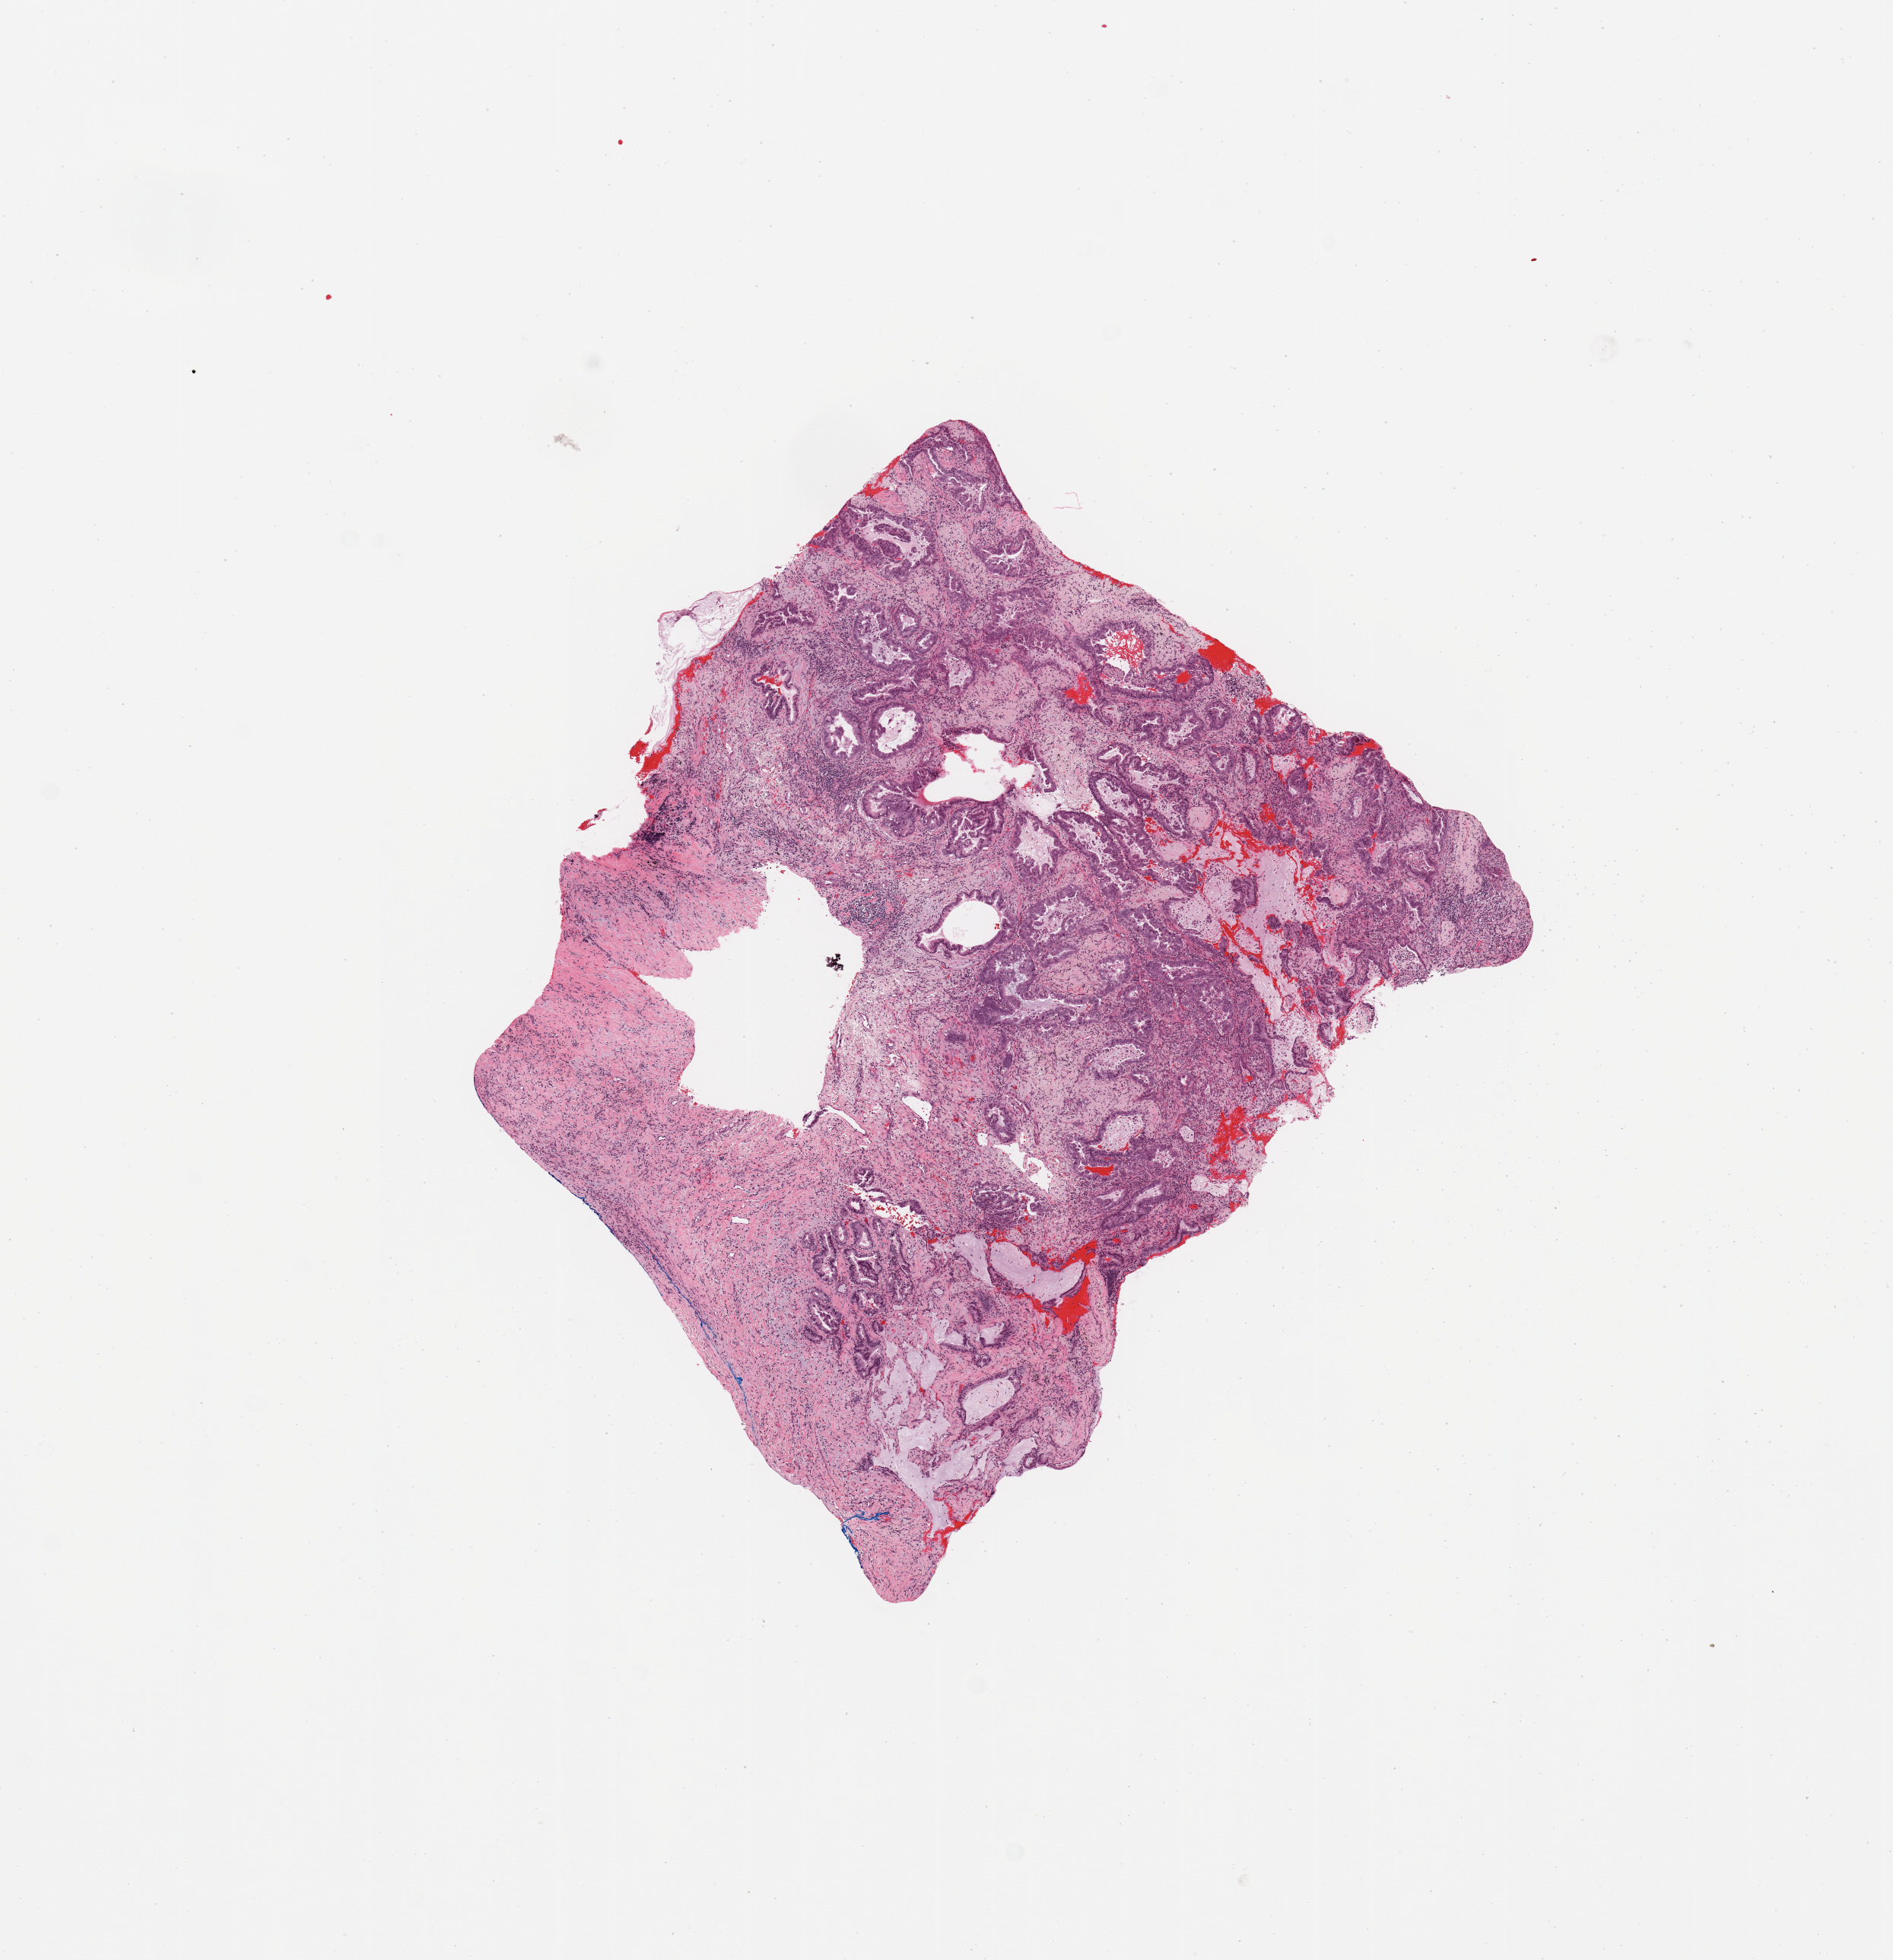
Whole-slide histology image, H&E, shown as a low-resolution overview of the whole scanned area (about 9.8 x 10.2 mm, acquisition: 20x scan), lung, tumour tissue. 81-year-old male patient. Histologic grade: G2 (moderately differentiated).
AJCC pathologic stage: IIIA. Primary tumour site (as recorded): left lower lobe. Diagnosis: Adenocarcinoma, NOS.